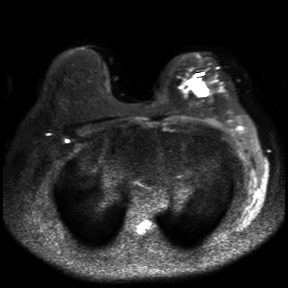
Breast MRI, one axial slice. Position 21 of 30 along the scan axis. Diffusion-weighted series; image 2 of 4 stored at this slice position (different b-values; order by instance number). 3 T. 4 mm slice thickness. 288 × 288 image matrix, field of view 360 × 360 mm. Female patient.
Structures marked on this image (expert manual segmentation):
- tumour on diffusion-weighted imaging: bounding box <189,78,208,96> (left, top, right, bottom; pixels)